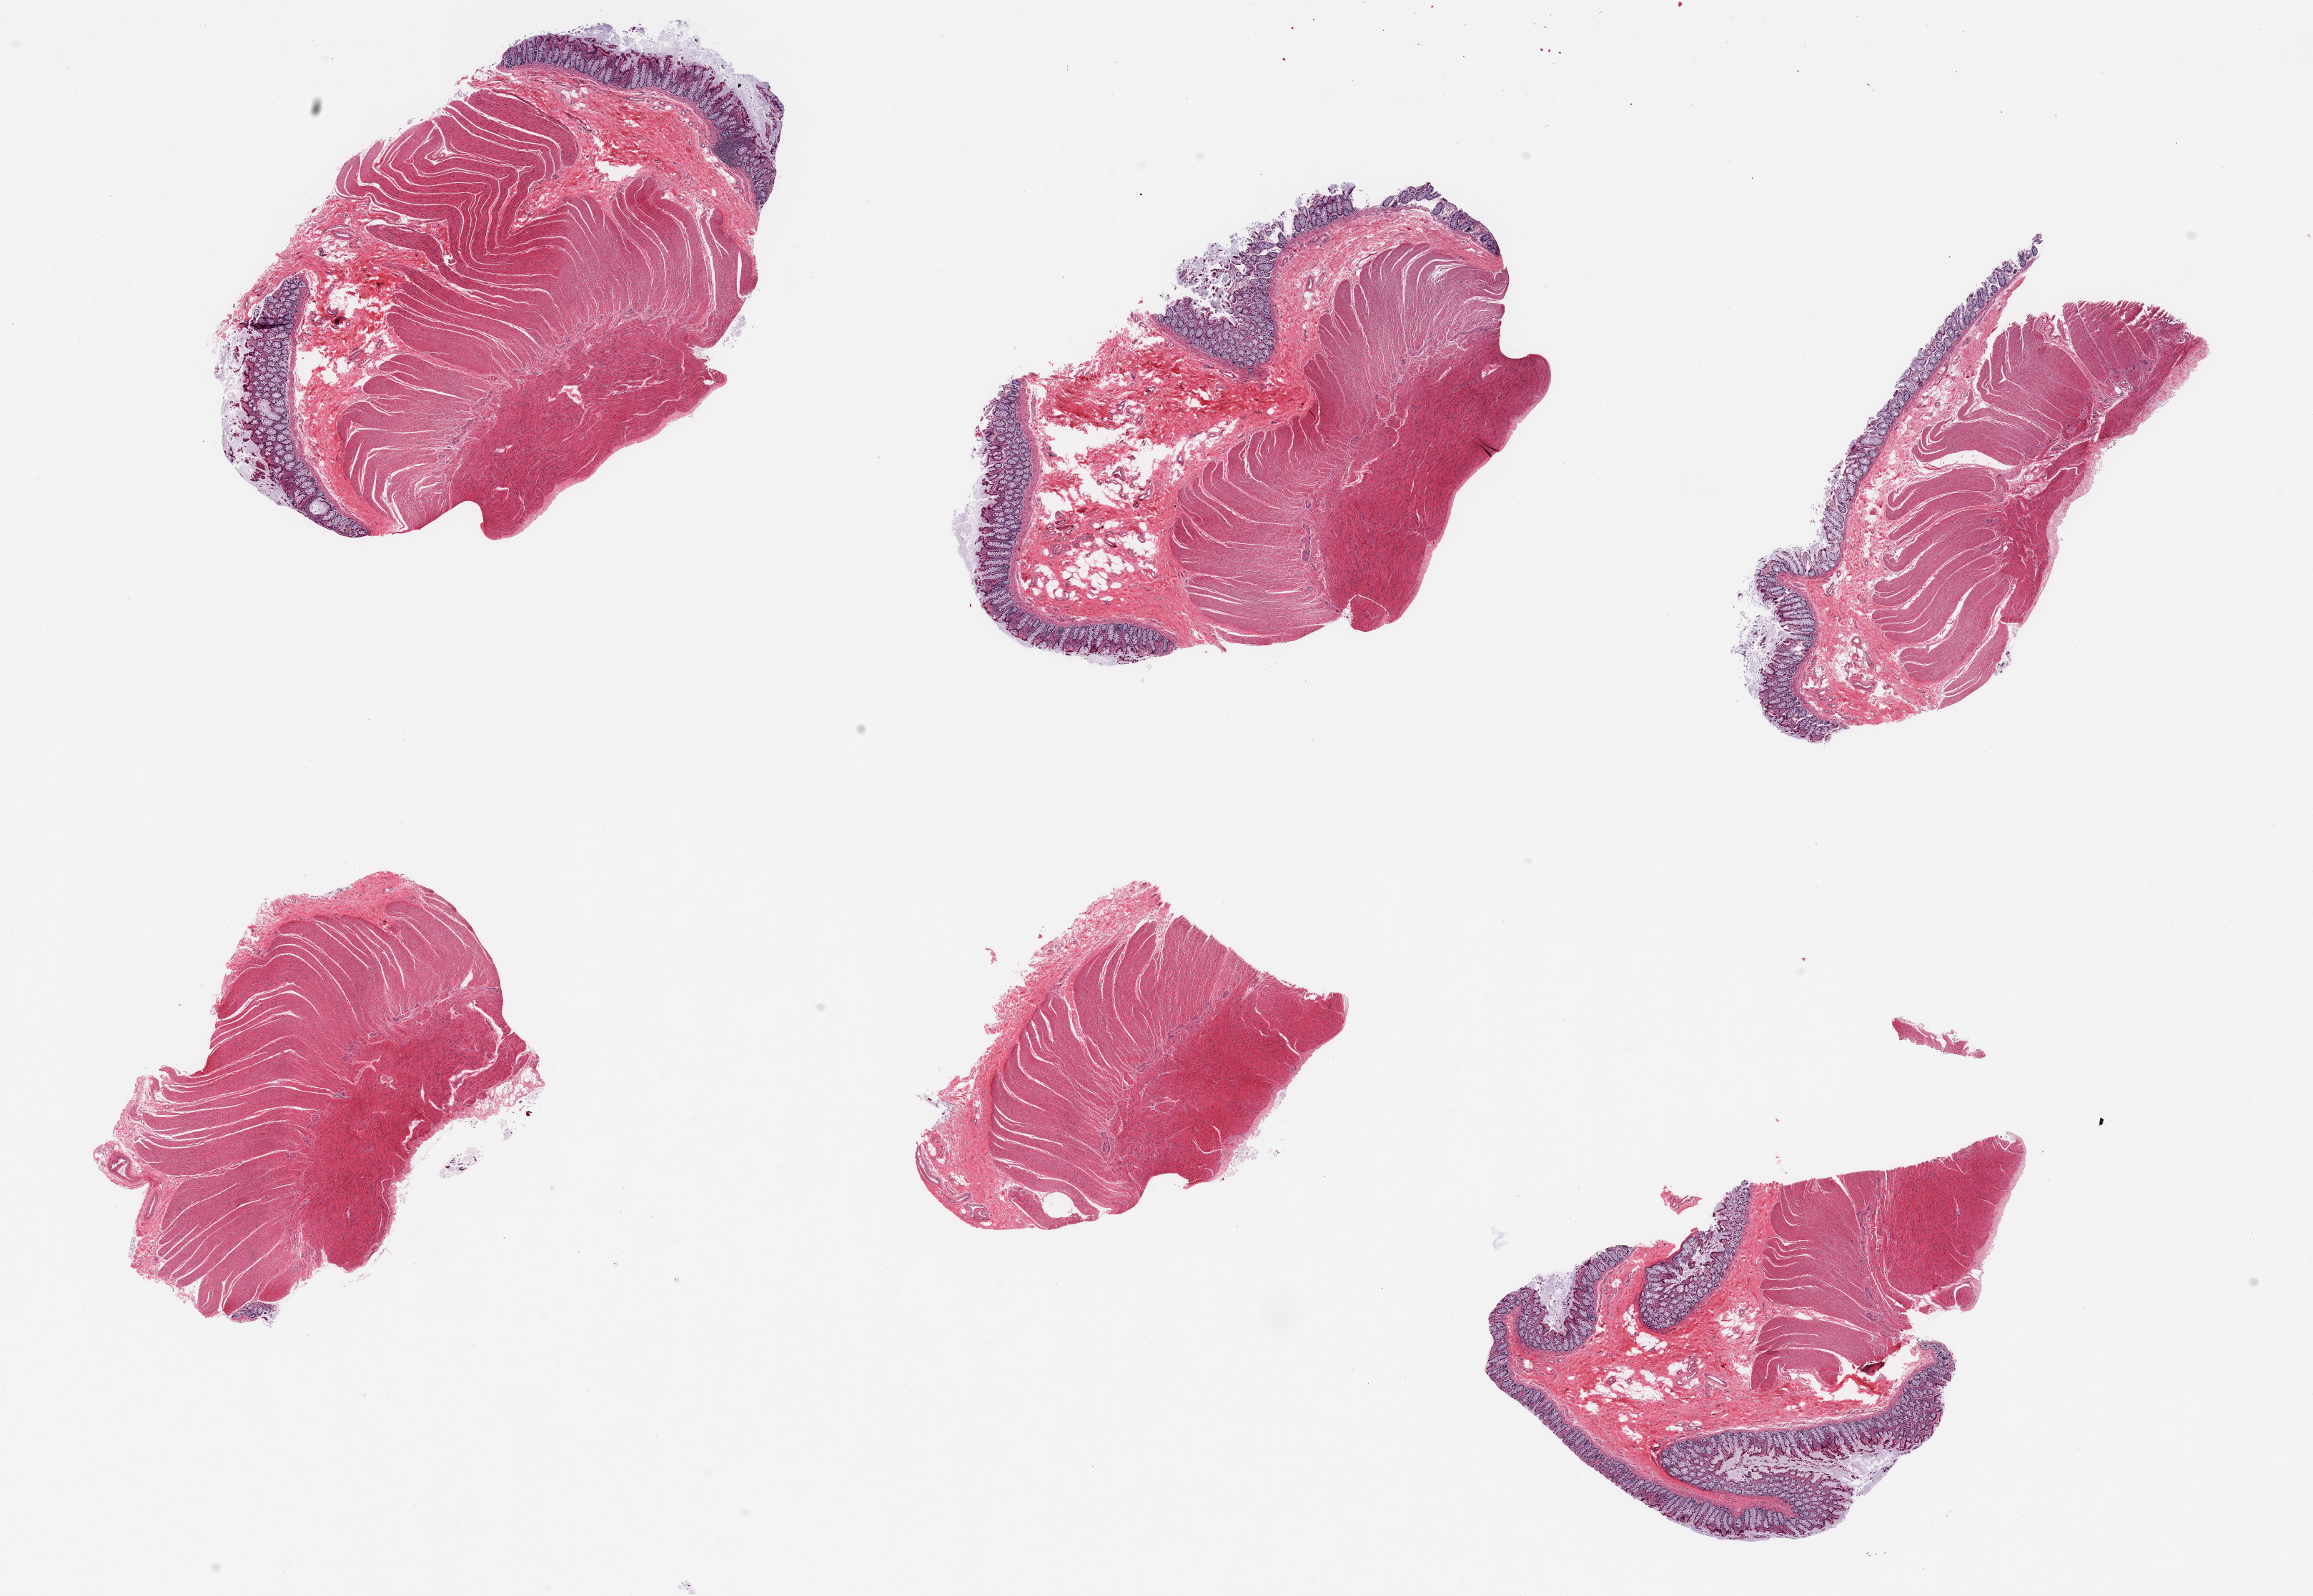
Digitized hematoxylin and eosin (H&E)-stained section, low-resolution overview of the scanned area, about 25.6 x 17.7 mm (acquisition: 20x scan); PAXgene-fixed paraffin-embedded (PFPE) section; sampled site (target tissue): sigmoid colon; donor tissue sample. Male donor.
Review note (as recorded): 6 pieces, target muscularis, ~10% 'contaminant mucosa up to ~0.3mm.